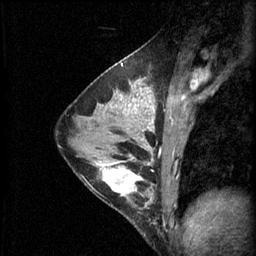
Breast MRI (dynamic contrast-enhanced), one sagittal slice; position 34 of 60 along the scan axis; 3 images stored at this slice position (order not interpretable as contrast timing); 1.5 T; TE 4.2 ms, TR 11 ms; 2.1 mm slice thickness; 256 × 256 image matrix, field of view 180 × 180 mm. Female patient, age 29 years.
Annotated regions visible in this slice (semi-automatic segmentation, software-assisted and operator-edited):
- analysis volume of interest (the breast-tissue region the enhancement analysis was run in; not a lesion): bounding box <95,164,153,227> (left, top, right, bottom; pixels)
- tumour enhancement mask (voxels above the 70 % enhancement threshold inside the analysis volume of interest): <101,164,149,197>